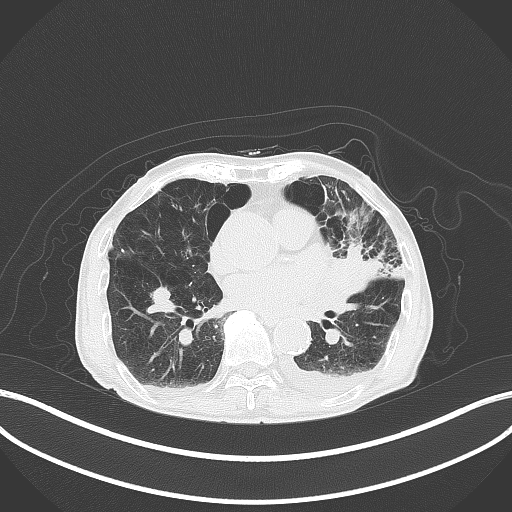
Chest CT, one axial slice; position 181 of 227 along the scan axis; reconstruction kernel B70f; lung window (W 1500 / L -600 HU); 3 mm slice thickness; 512 × 512 image matrix, field of view 400 × 400 mm. Male patient, age 90 years or older. From the clinical record (not read from this slice): clinical TNM (as recorded): T2b N1 M0.
Structures marked on this image (rectangle marked by the reading radiologist):
- lung tumour (recorded histology: squamous cell carcinoma): bounding box [x1, y1, x2, y2] px = [318, 240, 398, 303]